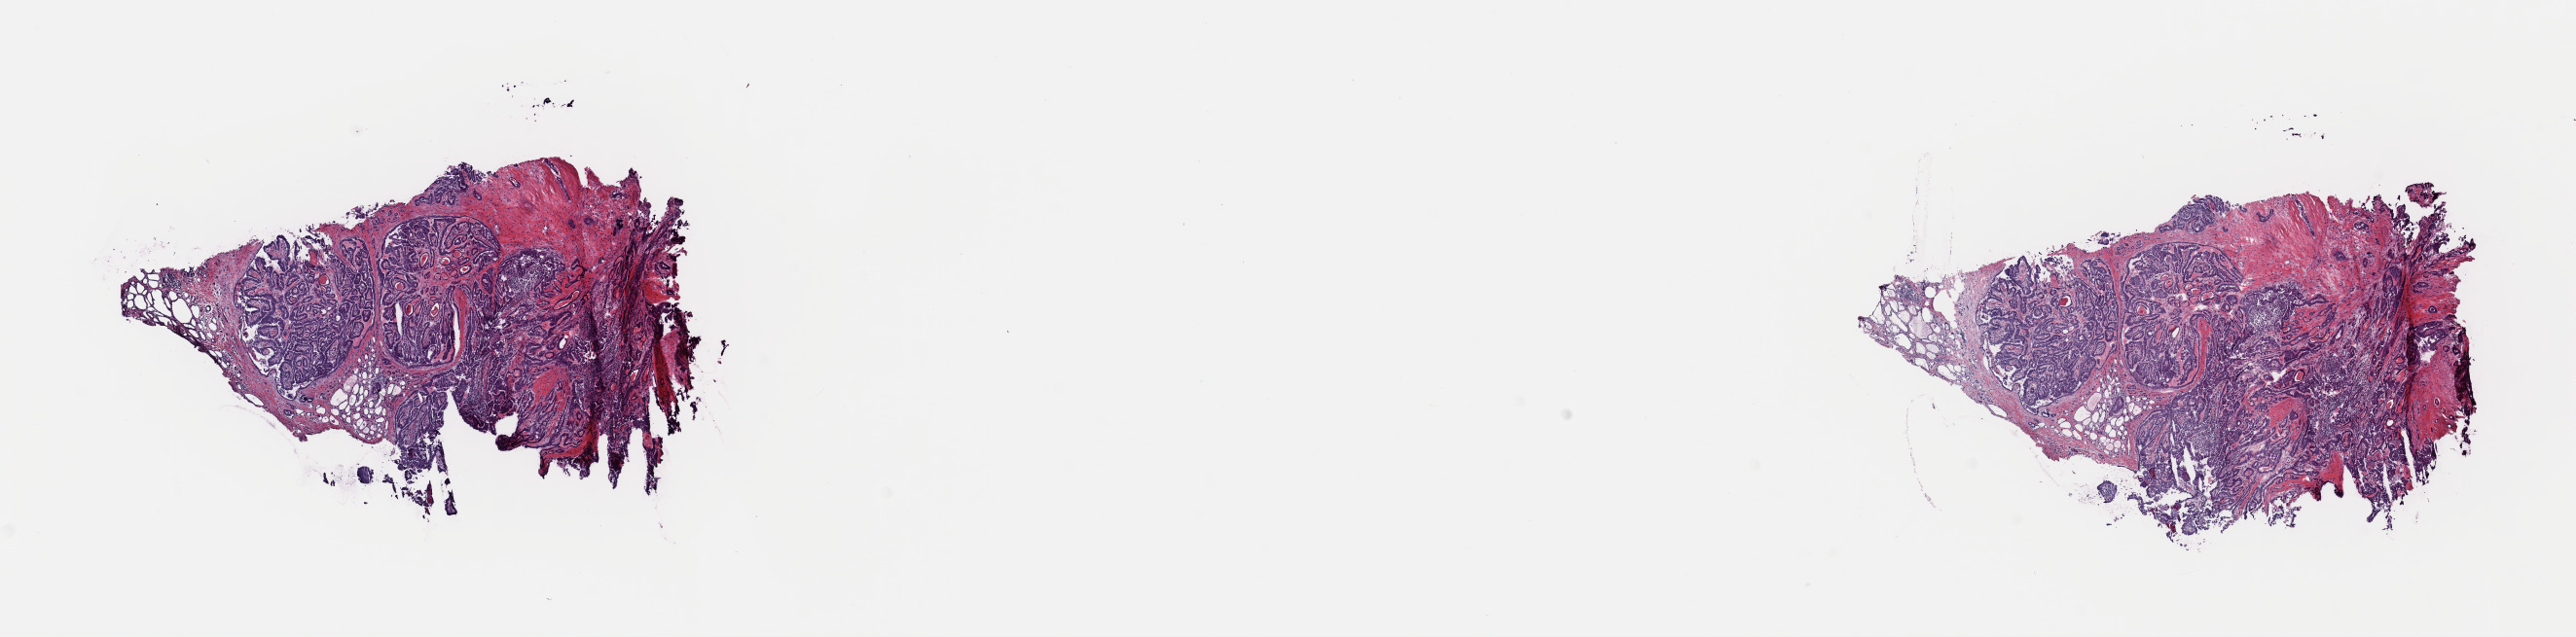
Whole-slide histology image, H&E, a low-resolution overview of the entire scanned area, about 20.9 x 5.2 mm (slide scanned at 40x), frozen section, sample: primary tumour, thyroid. Patient: female, age at initial diagnosis 53 years. Pathologist review of this section (percent, as recorded): tumour cells 90%, tumour nuclei 90%, normal cells 5%, stromal cells 5%, necrosis 0%. Inflammatory infiltration, as recorded: lymphocyte infiltration 0%, monocyte infiltration 0%, neutrophil infiltration 0%.
* AJCC pathologic stage: IVA (7th edition)
* TNM: T2 N1b M0
* diagnosis: Papillary adenocarcinoma, NOS (thyroid gland)
* laterality: bilateral